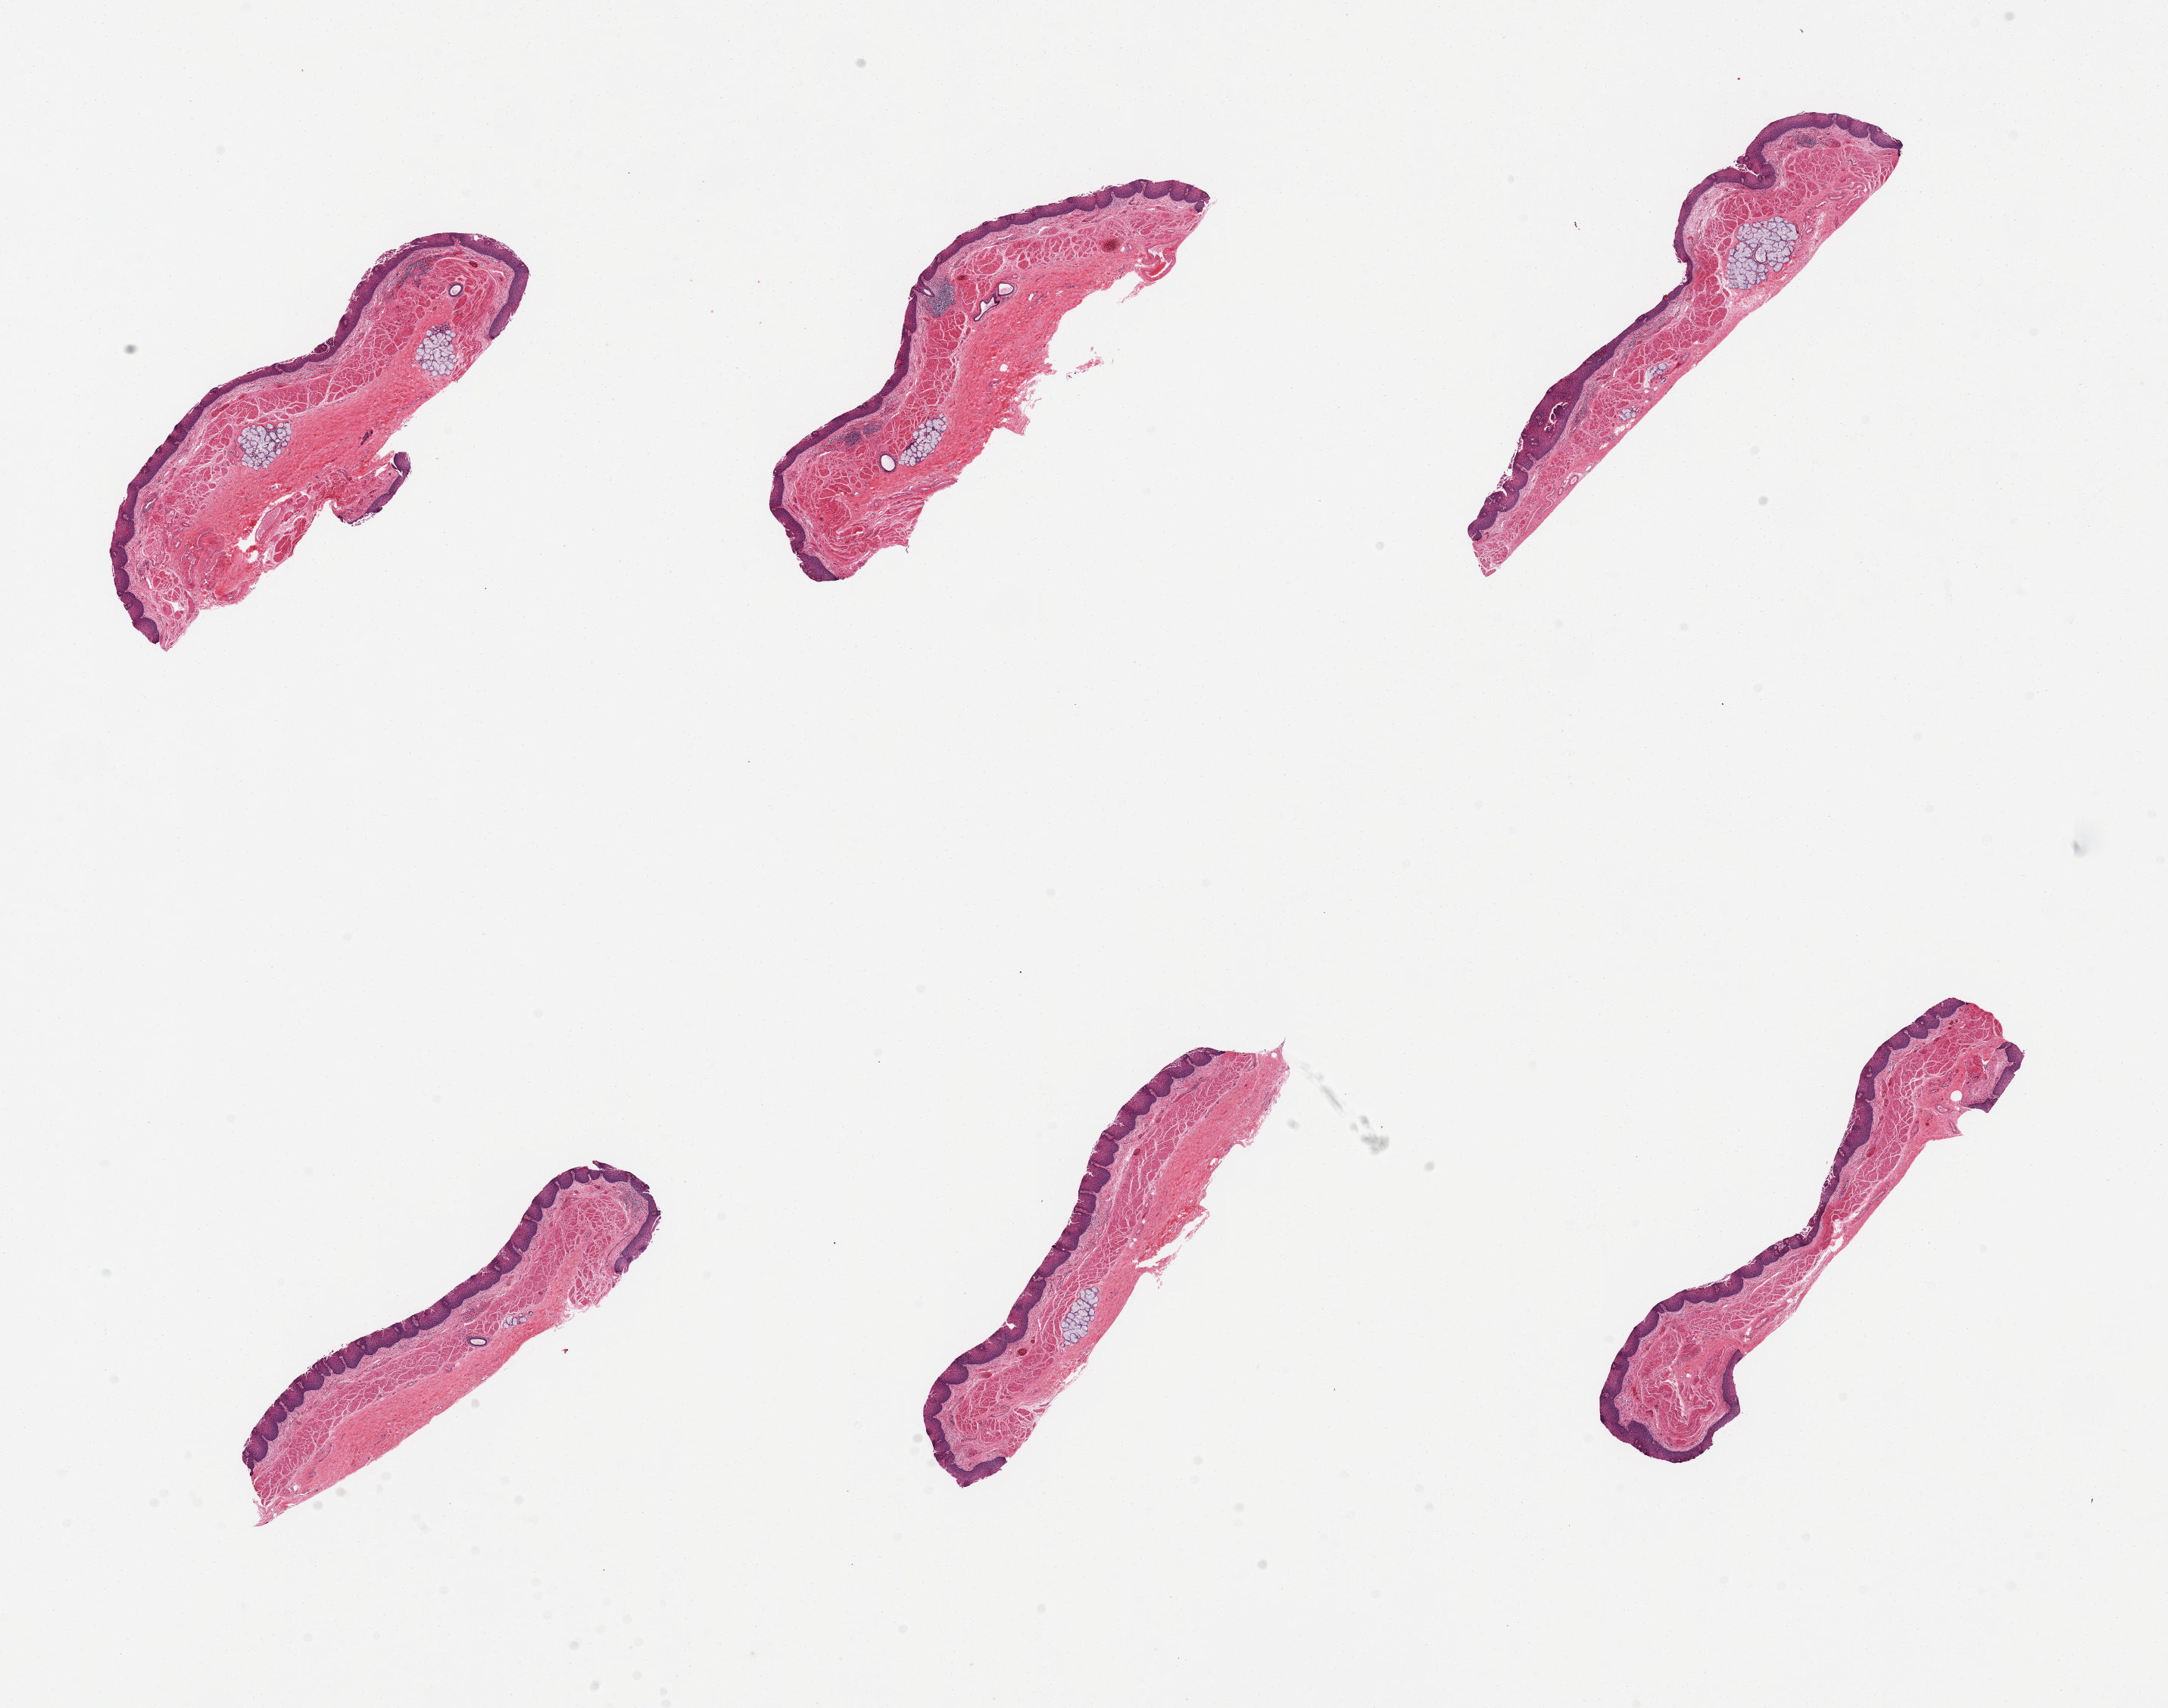
Digitized H&E-stained section, brightfield, low-resolution overview of the scanned area, about 22.6 x 17.8 mm; PAXgene-fixed paraffin-embedded (PFPE) section; target tissue: esophageal mucous membrane; tissue donor sample. Male donor.
Reviewer comment on this tissue sample: 6 pieces, squamous mucosa is ~0.2mm, ~15% thickness. Focally early superficial sloughing is beginning (ie, early score'2;).